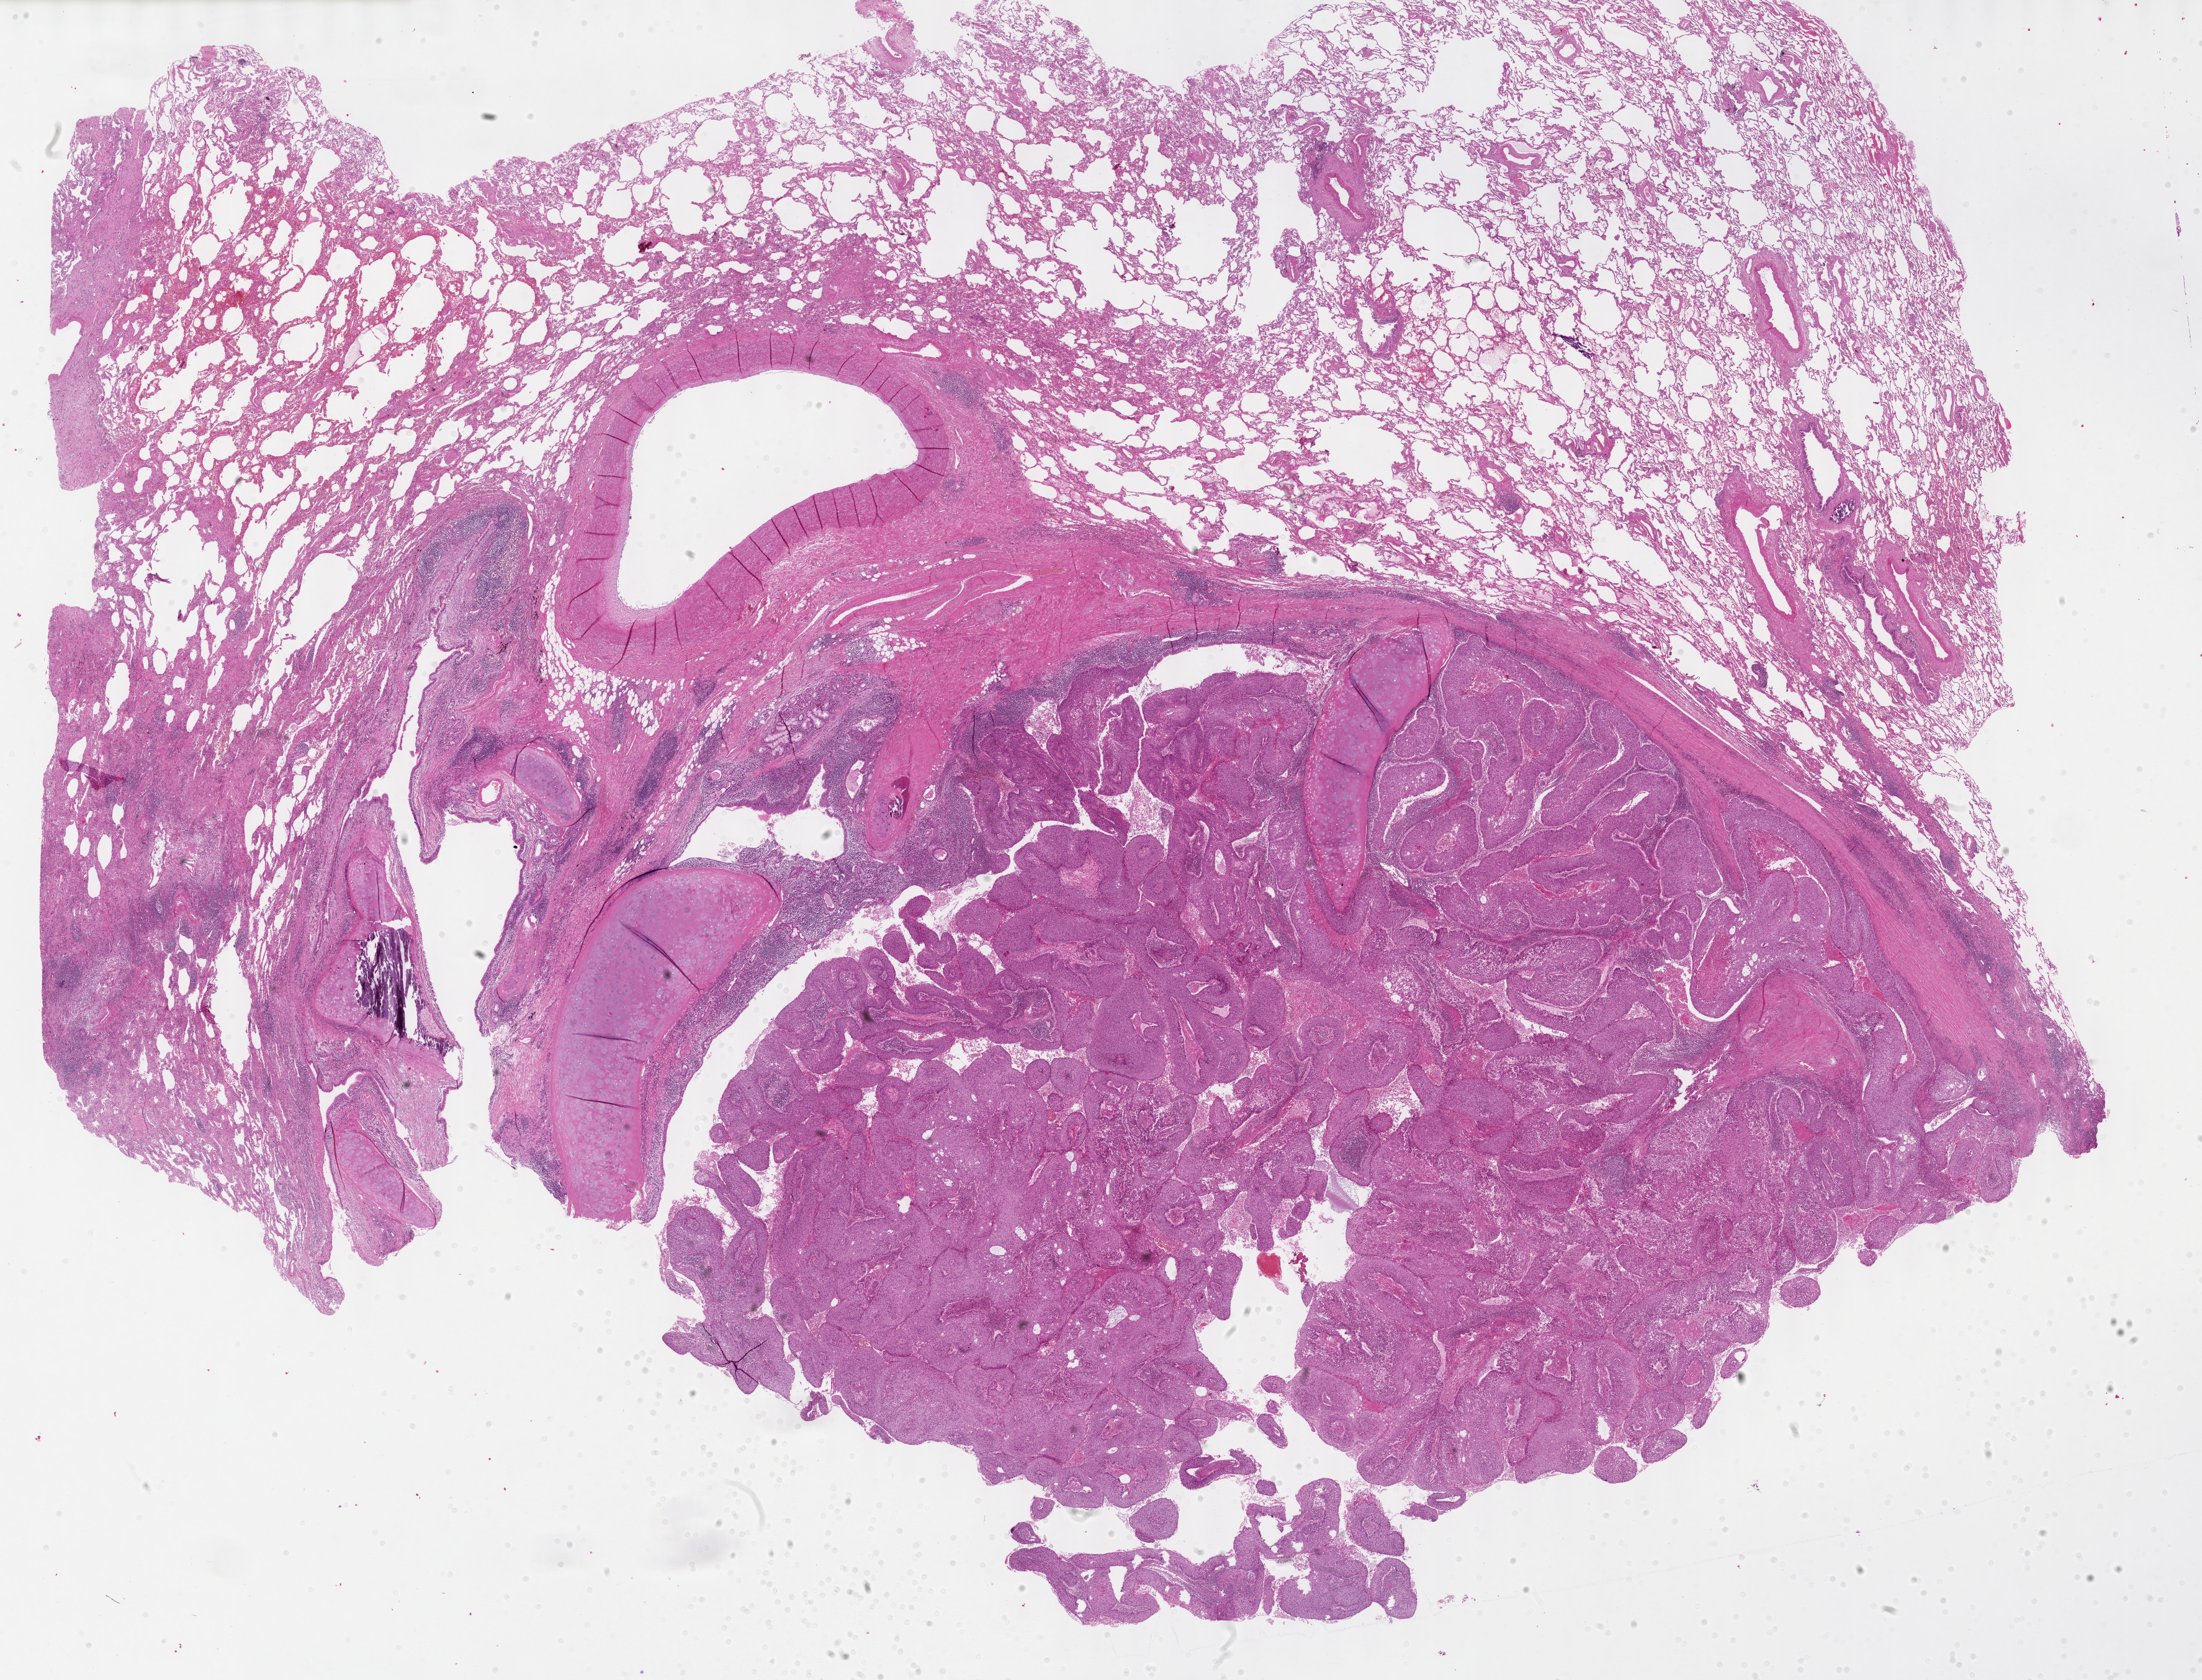
Whole-slide histology image, H&E-stained — low-resolution overview of the scanned area, about 28.7 x 21.9 mm; FFPE section; lung, primary tumour sample. Male, age 77 years at initial diagnosis.
* pathologic diagnosis: Squamous cell carcinoma, NOS (lower lobe, lung)
* AJCC pathologic stage: IIA (7th edition)